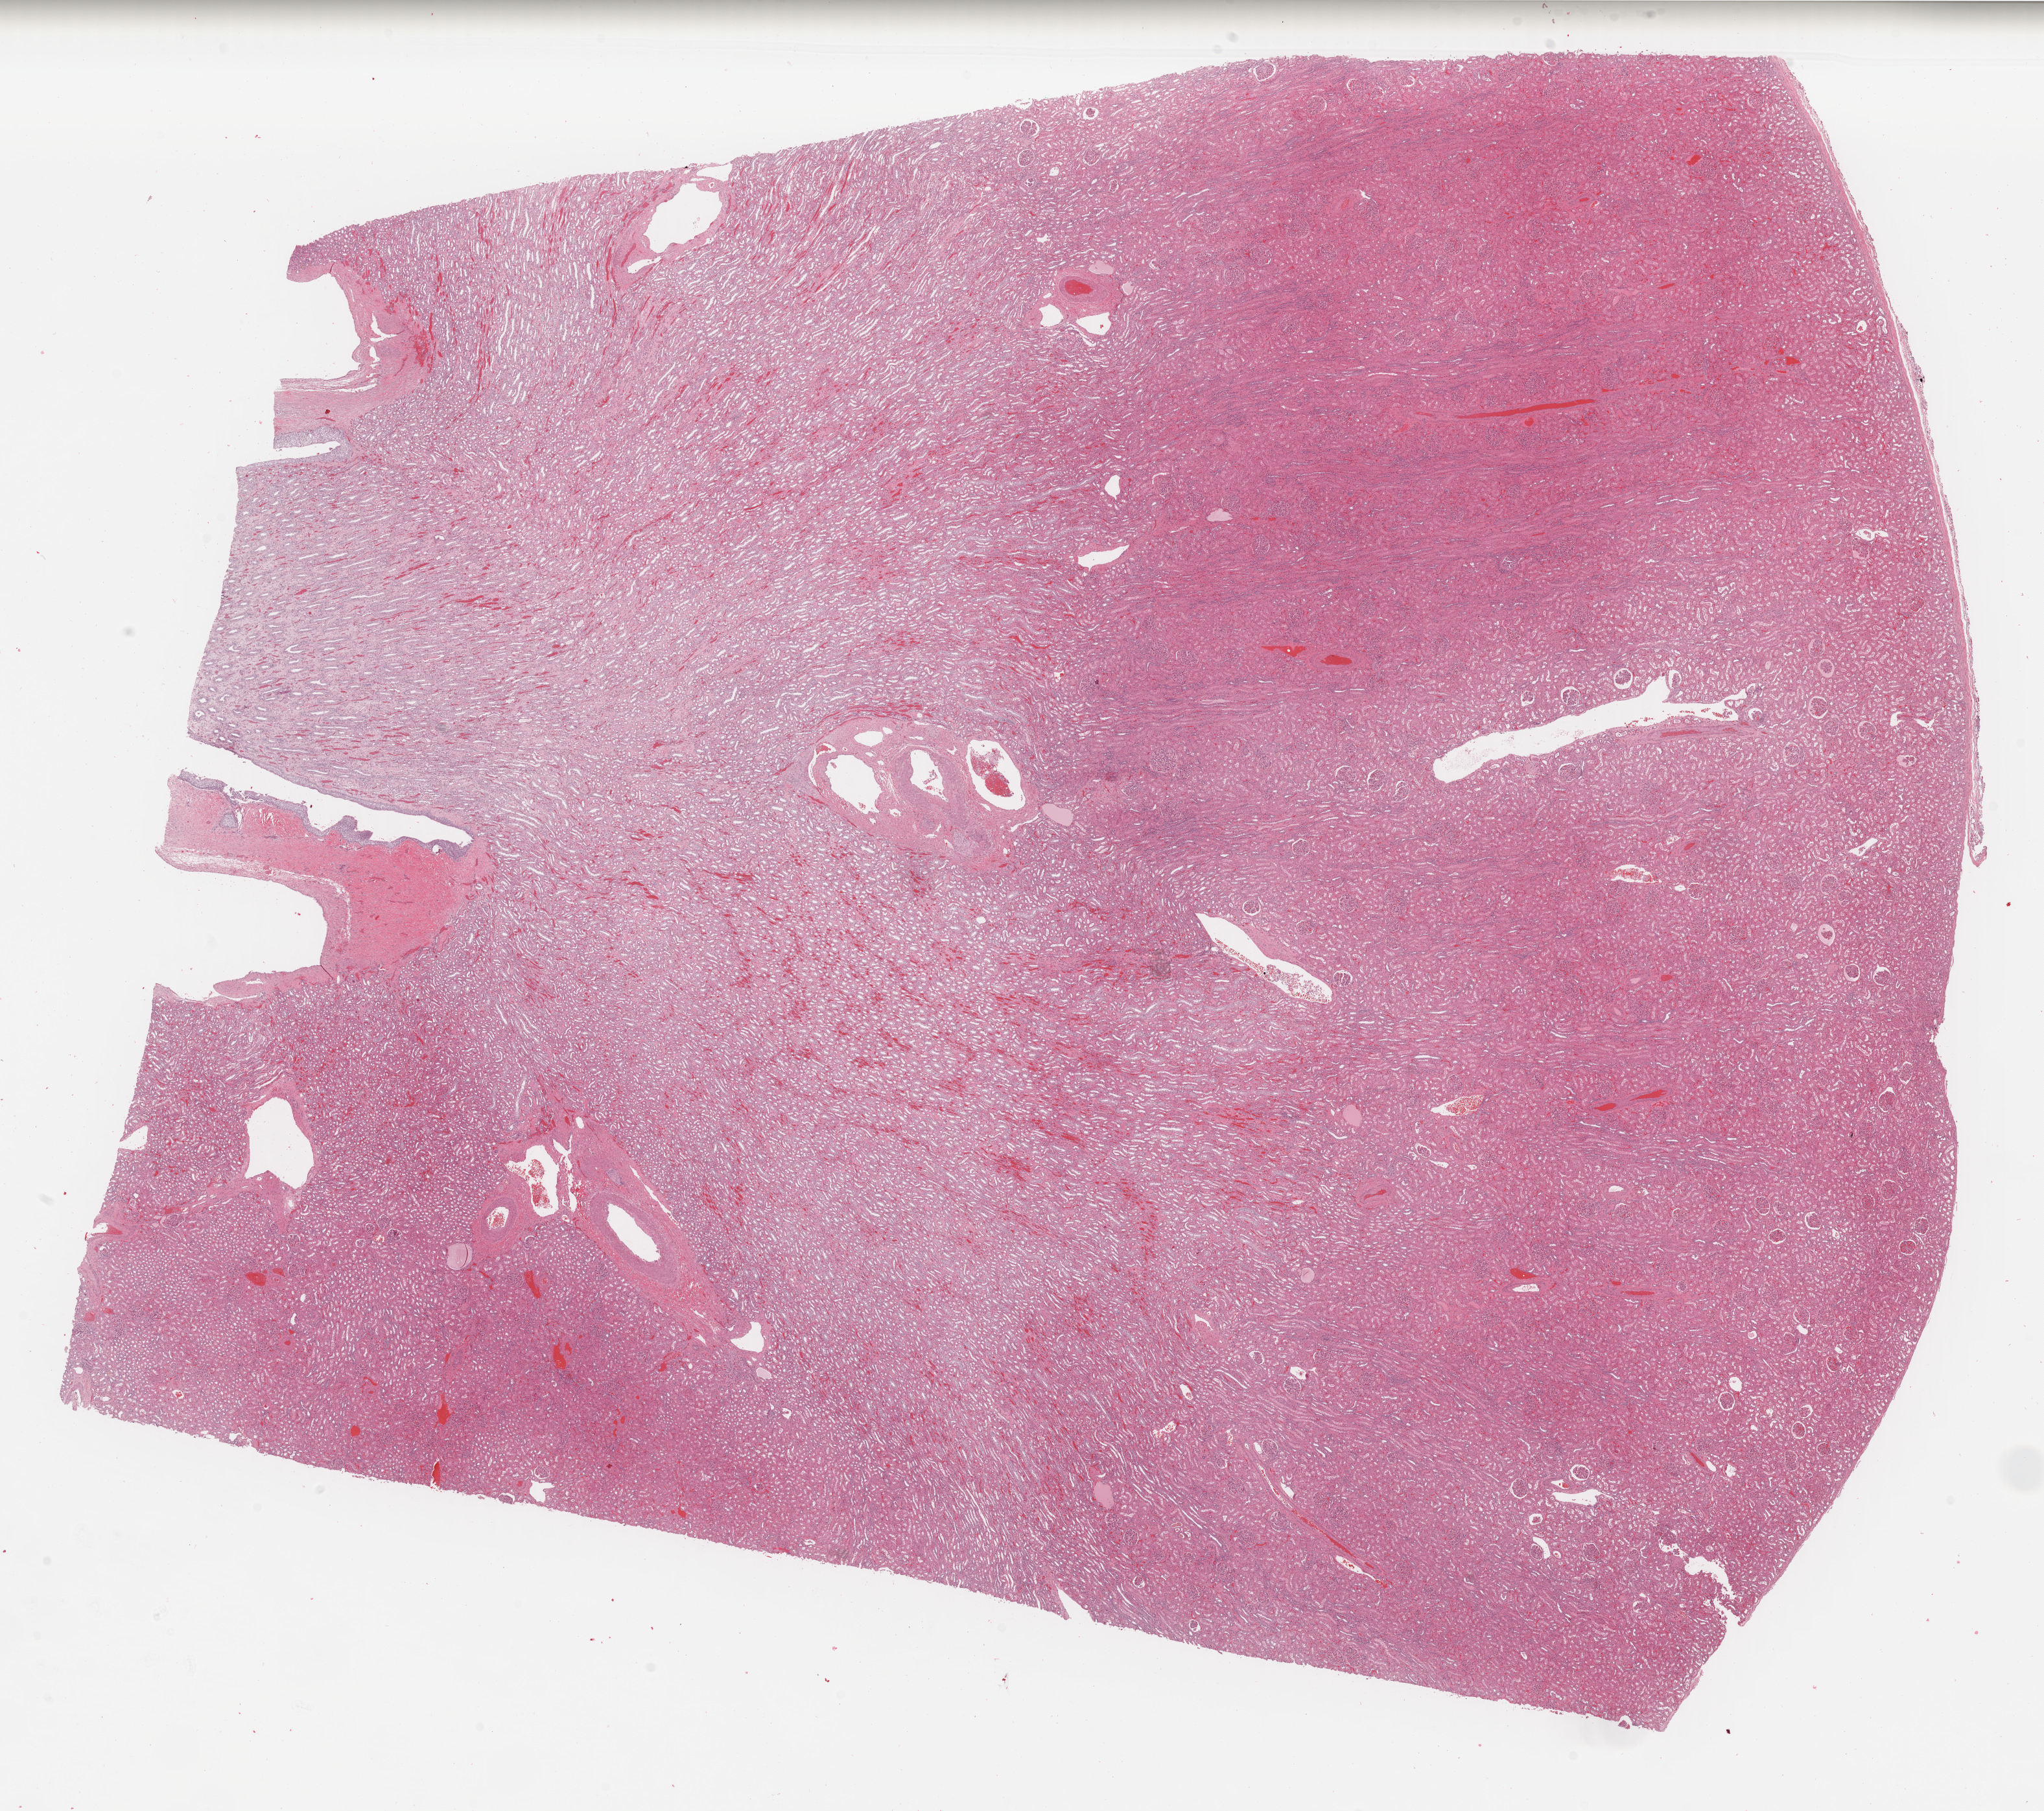
Whole-slide histology image, H&E, low-resolution overview of the scanned area, about 24.9 x 22.1 mm (slide scanned at 40x), formalin-fixed paraffin-embedded (FFPE) diagnostic section, solid tissue normal (non-tumour tissue) sample from the kidney. Male, age 47 years at initial diagnosis.
This section: solid tissue normal (non-tumour) sample from the same patient. Patient diagnosis: Renal cell carcinoma, chromophobe type.